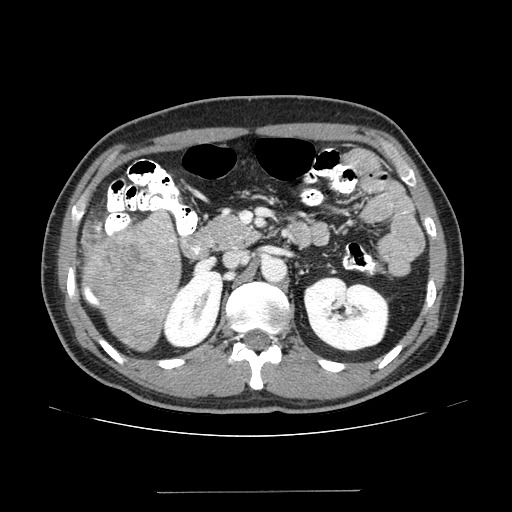
Contrast-enhanced abdominal CT (liver protocol), one axial slice. Position 65 of 131 along the scan axis. Reconstruction kernel STANDARD. 100 kVp. One of 2 acquisitions stored at this slice position. Soft-tissue window (W 400 / L 40 HU). 2.5 mm slice thickness. 512 × 512 image matrix, field of view 380 × 380 mm. Case-level facts recorded for this patient, not image findings: diagnosis: hepatocellular carcinoma (patient treated with transarterial chemoembolisation; whether this scan precedes or follows treatment is not stated here); TNM stage (as recorded): Stage-I; Child-Pugh class: A; tumour differentiation: poorly differentiated; tumour nodularity: uninodular.
Structures marked on this image (semi-automatically segmented with operator editing):
- liver parenchyma outside the tumour (the mass and vessels are separate outlines, so this box may not span the whole liver): bounding box <82,212,180,350> (left, top, right, bottom; pixels)
- mass: <89,228,162,304>
- liver vessels: <85,288,98,304>